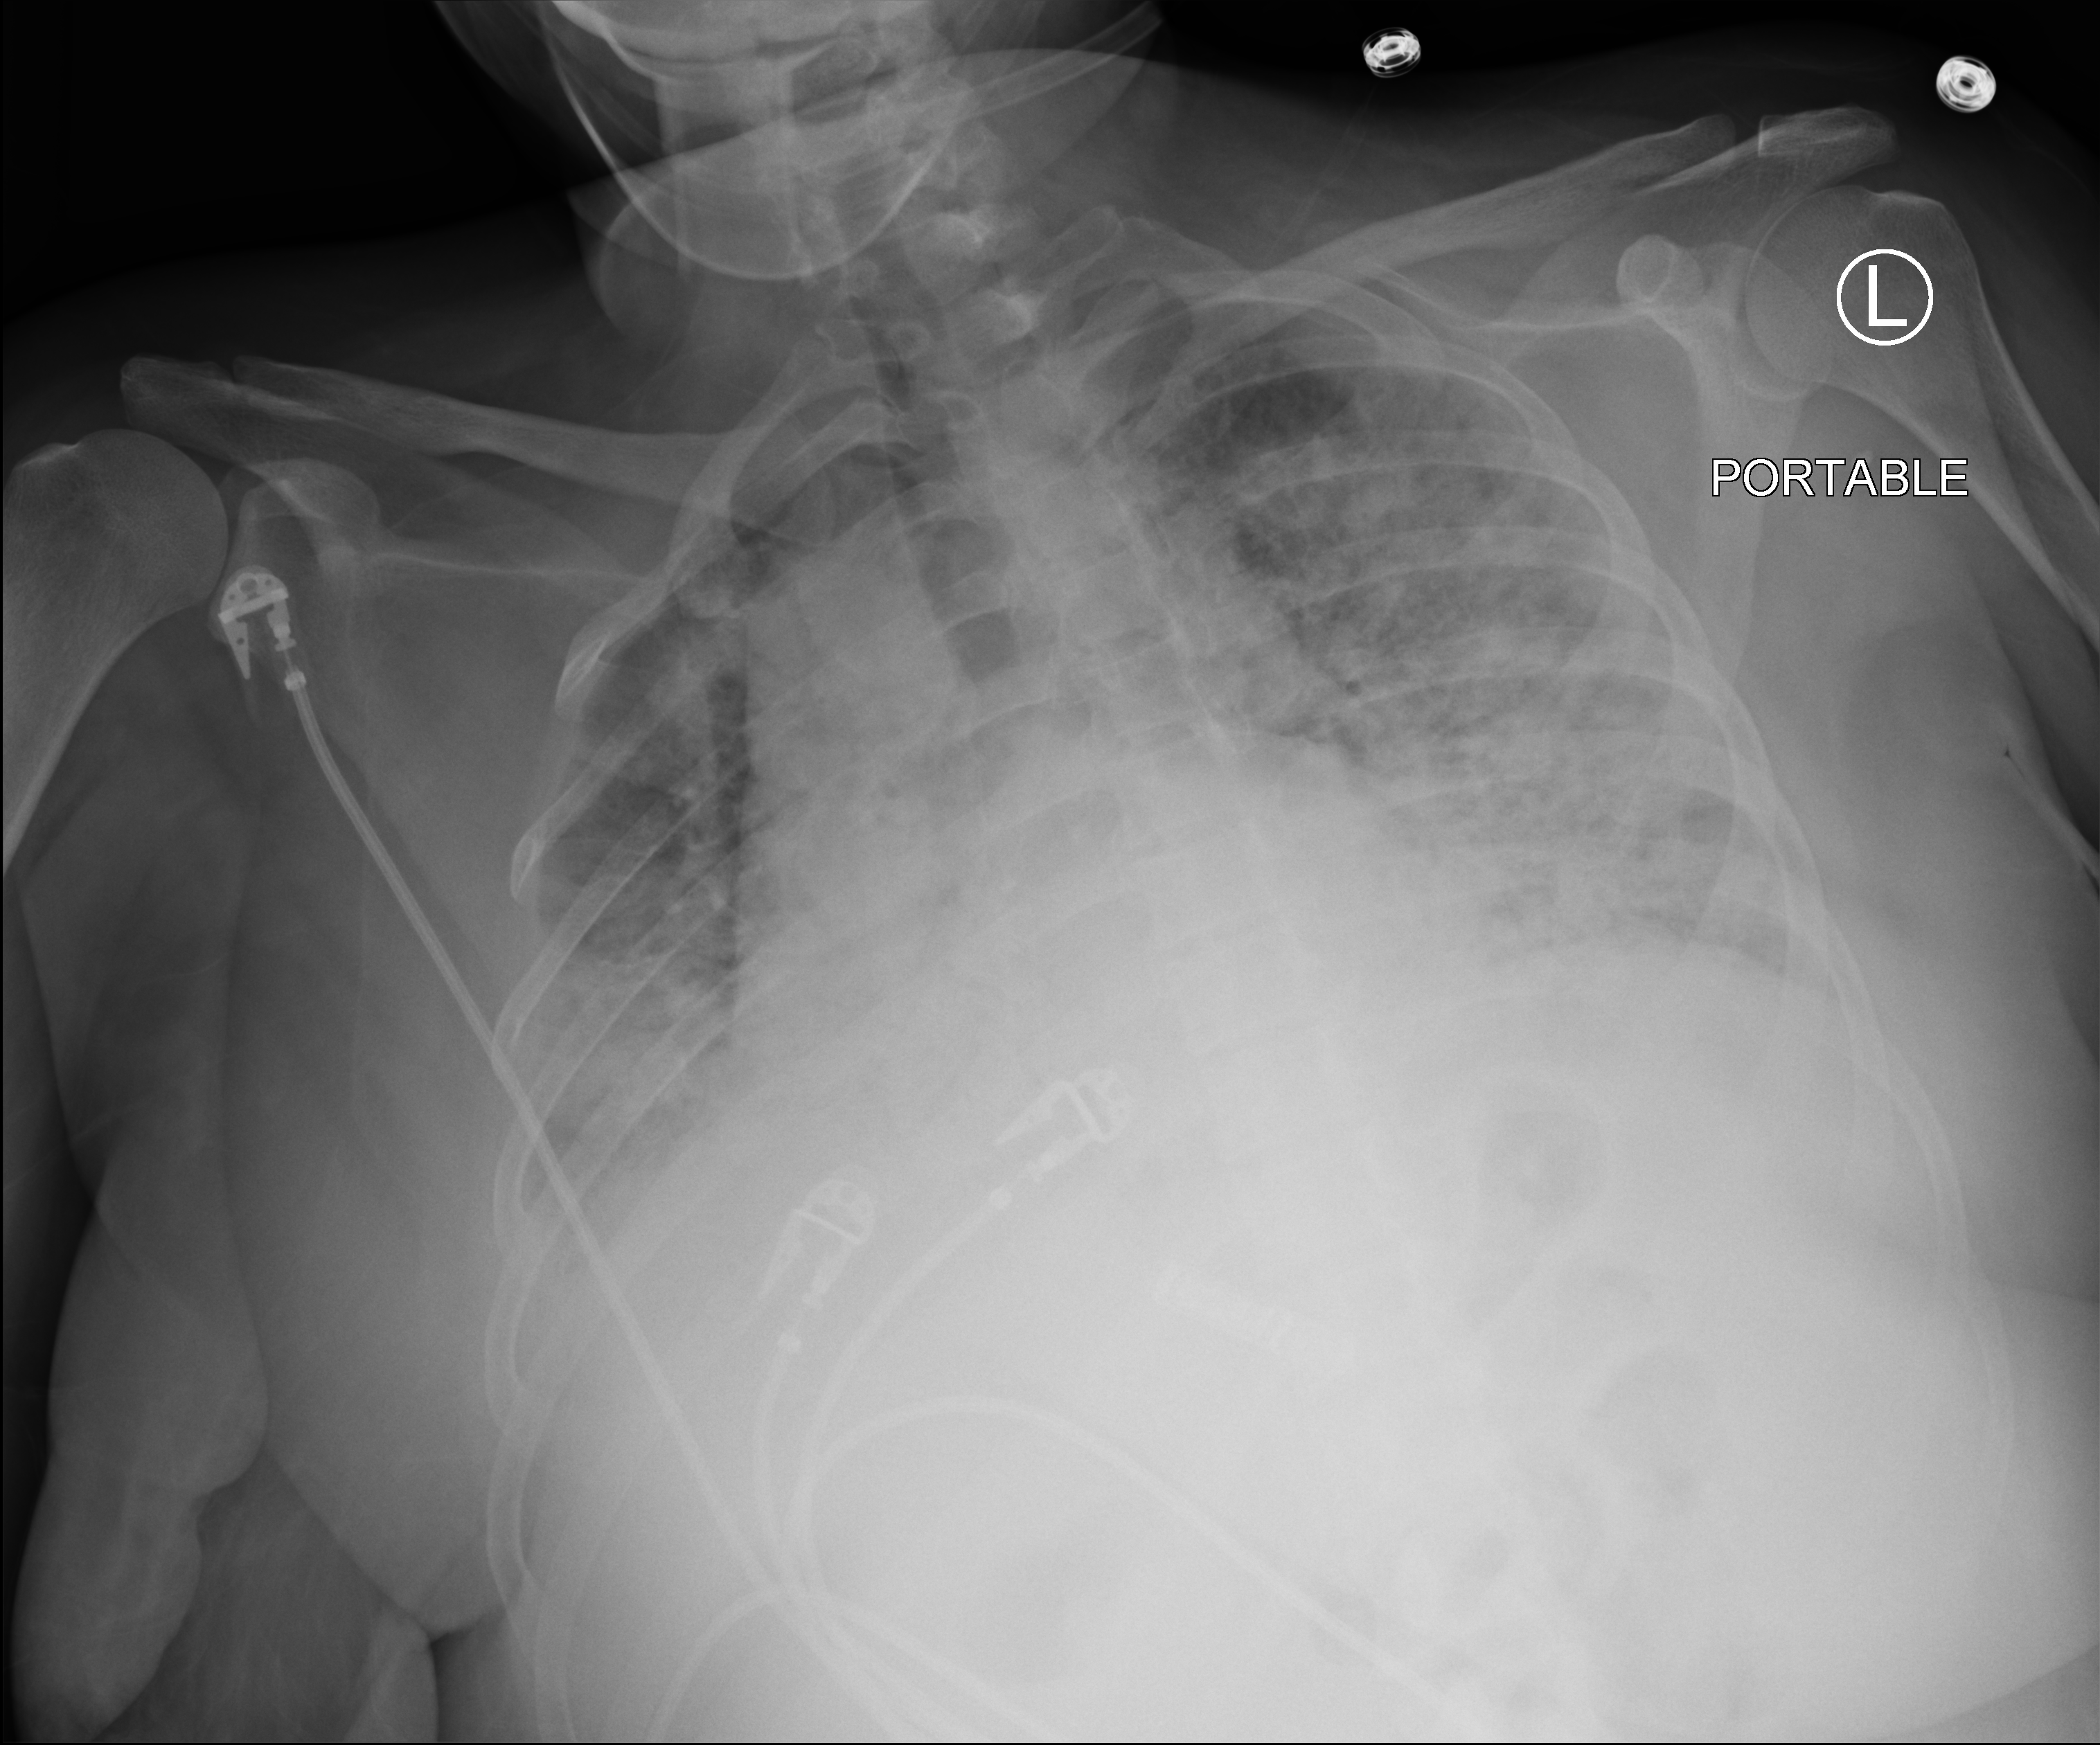
Bedside chest radiograph (computed radiography); anteroposterior (AP) projection. Patient hospitalised with COVID-19; female, aged 18–59 years.
Hospital-stay facts (about this admission, not read from this image; timing relative to this image not recorded): length of hospital stay: 33 days; admitted to intensive care during this hospital stay: no; mechanically ventilated during this hospital stay: yes.